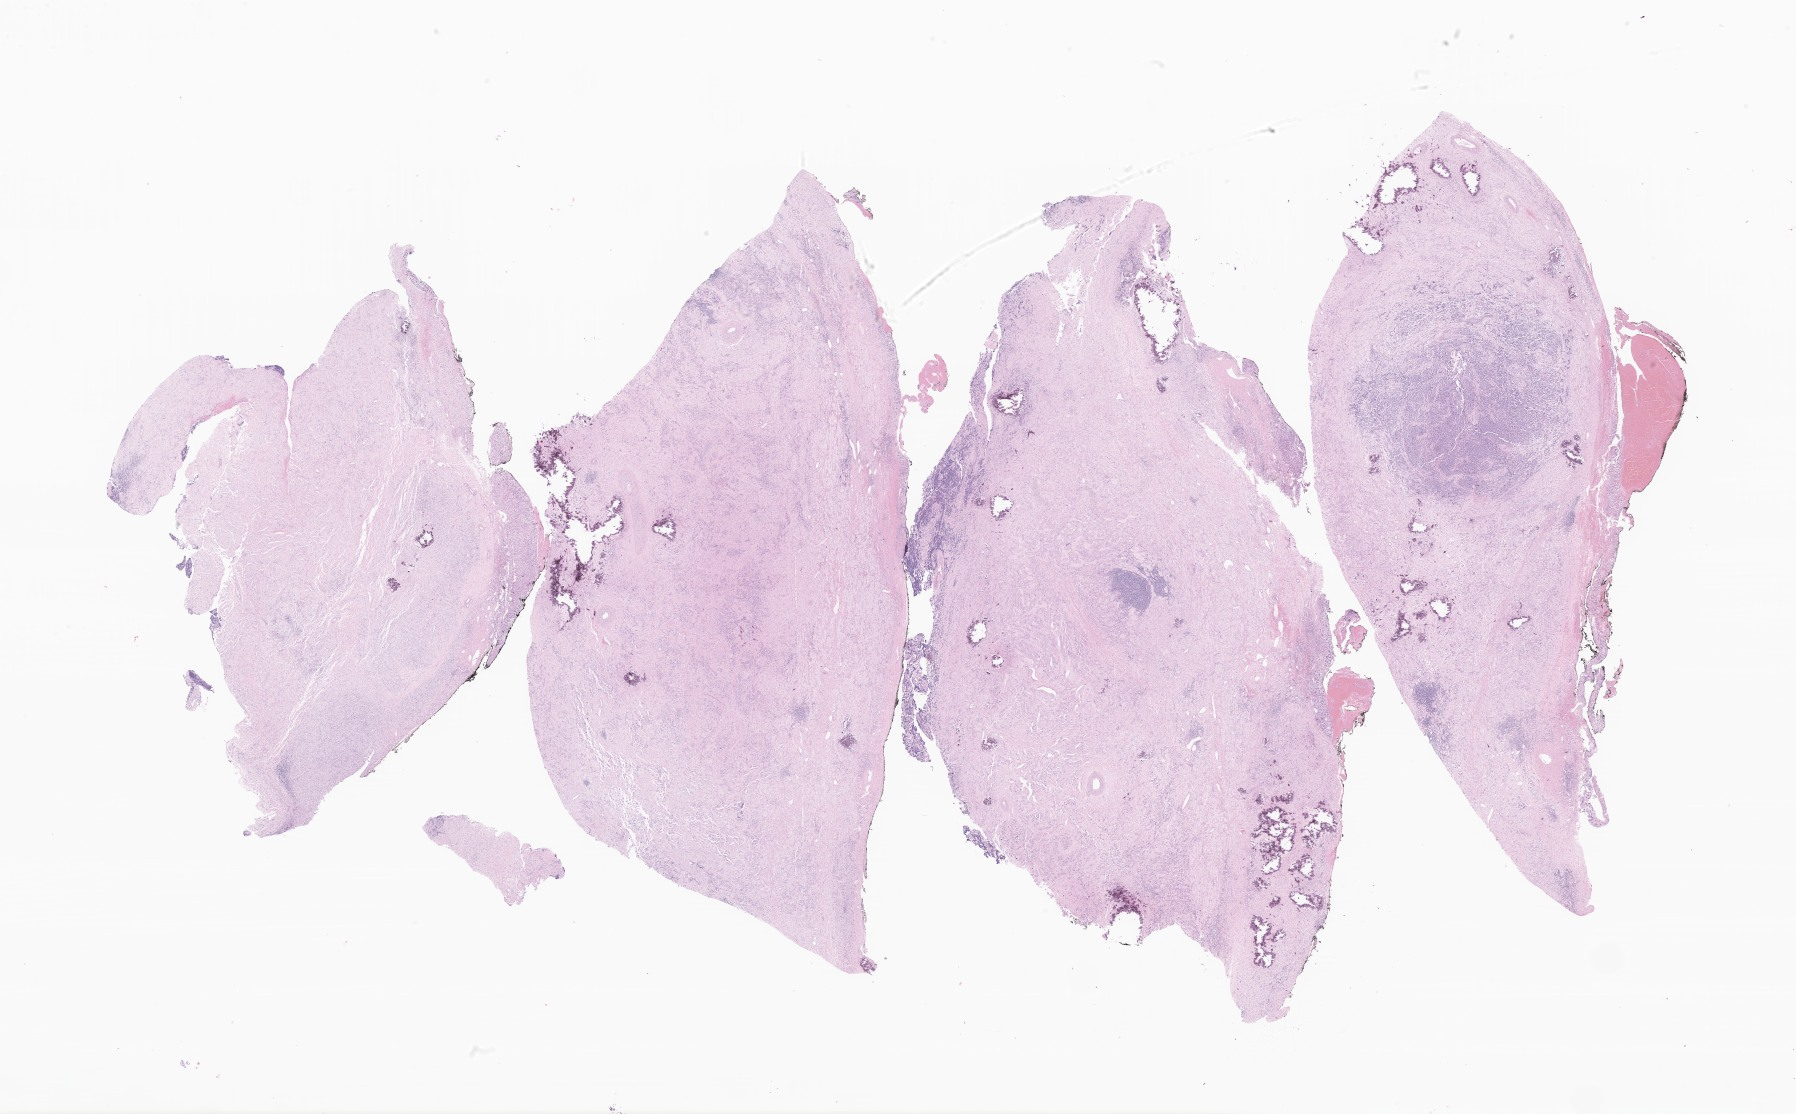
Whole-slide image, H&E stain of tumor tissue from the pelvis, a low-resolution overview of the entire scanned area, about 30.3 x 18.8 mm. FFPE section. Patient male; age 34 months (2 years 10 months).
Diagnosis (ICD-O-3 morphology term): Neuroblastoma, NOS.